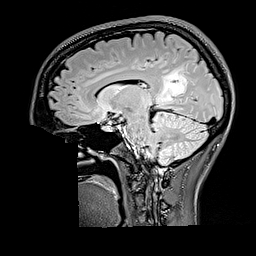
Brain MRI from a brain-tumour surgery series, one sagittal slice; T2 FLAIR; 256 × 256 image matrix. Case-level facts recorded for this patient, not image findings: histopathology: Oligodendroglioma; WHO grade: 2; IDH mutation: yes; tumour location: Right Parietal.
Structures marked on this image (outlined manually by an expert reader):
- tumour: bounding box <160,67,188,104> (left, top, right, bottom; pixels)